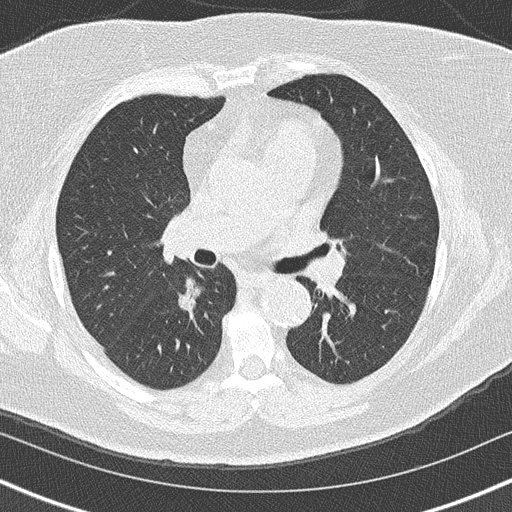
Axial slice from a low-dose chest CT screening exam; second screening round (one year after baseline); lung window (W 1500 / L -600 HU); 2 mm slice thickness; lung (sharp) reconstruction kernel (B50f); 512 × 512 image matrix, field of view 320 × 320 mm. Female participant, aged 60 years at enrolment. Former smoker at enrolment.
- Lesion marked by an expert reader, bounding box [x1, y1, x2, y2] px = [150, 267, 216, 324].
- Reader record for this screening exam (exam-level; its link to the box is not recorded): non-calcified nodule or mass ≥4 mm, right lower lobe, 20 × 19 mm, soft tissue attenuation, pre-existing on the prior screen: yes; interval growth: yes.
- Official screen result: positive, other.